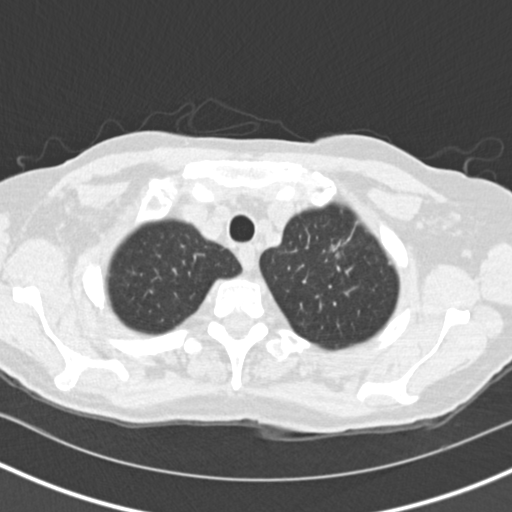
Chest CT (low-dose screening protocol), one axial image, baseline annual screen, lung window (W 1500 / L -600 HU), 2 mm slice thickness, standard (soft-tissue) reconstruction kernel (B30f), 120 kVp, slice 21 of 146 in the series, 512 × 512 image matrix. Female, age 73 years at enrolment. Current smoker at enrolment.
Lesion marked by an expert reader, bounding box [x1, y1, x2, y2] px = [307, 232, 357, 290]. The exam's reader record, not a measurement of the box and not confirmed to be the same lesion: non-calcified nodule or mass ≥4 mm, left upper lobe, 27 × 21 mm, spiculated (stellate) margins, soft tissue attenuation. Participant outcome: lung cancer diagnosed 72 days after this screen — bronchiolo-alveolar adenocarcinoma, NOS, left upper lobe, moderately differentiated (G2), stage IIIB (AJCC 6th edition), 17 mm at pathology.